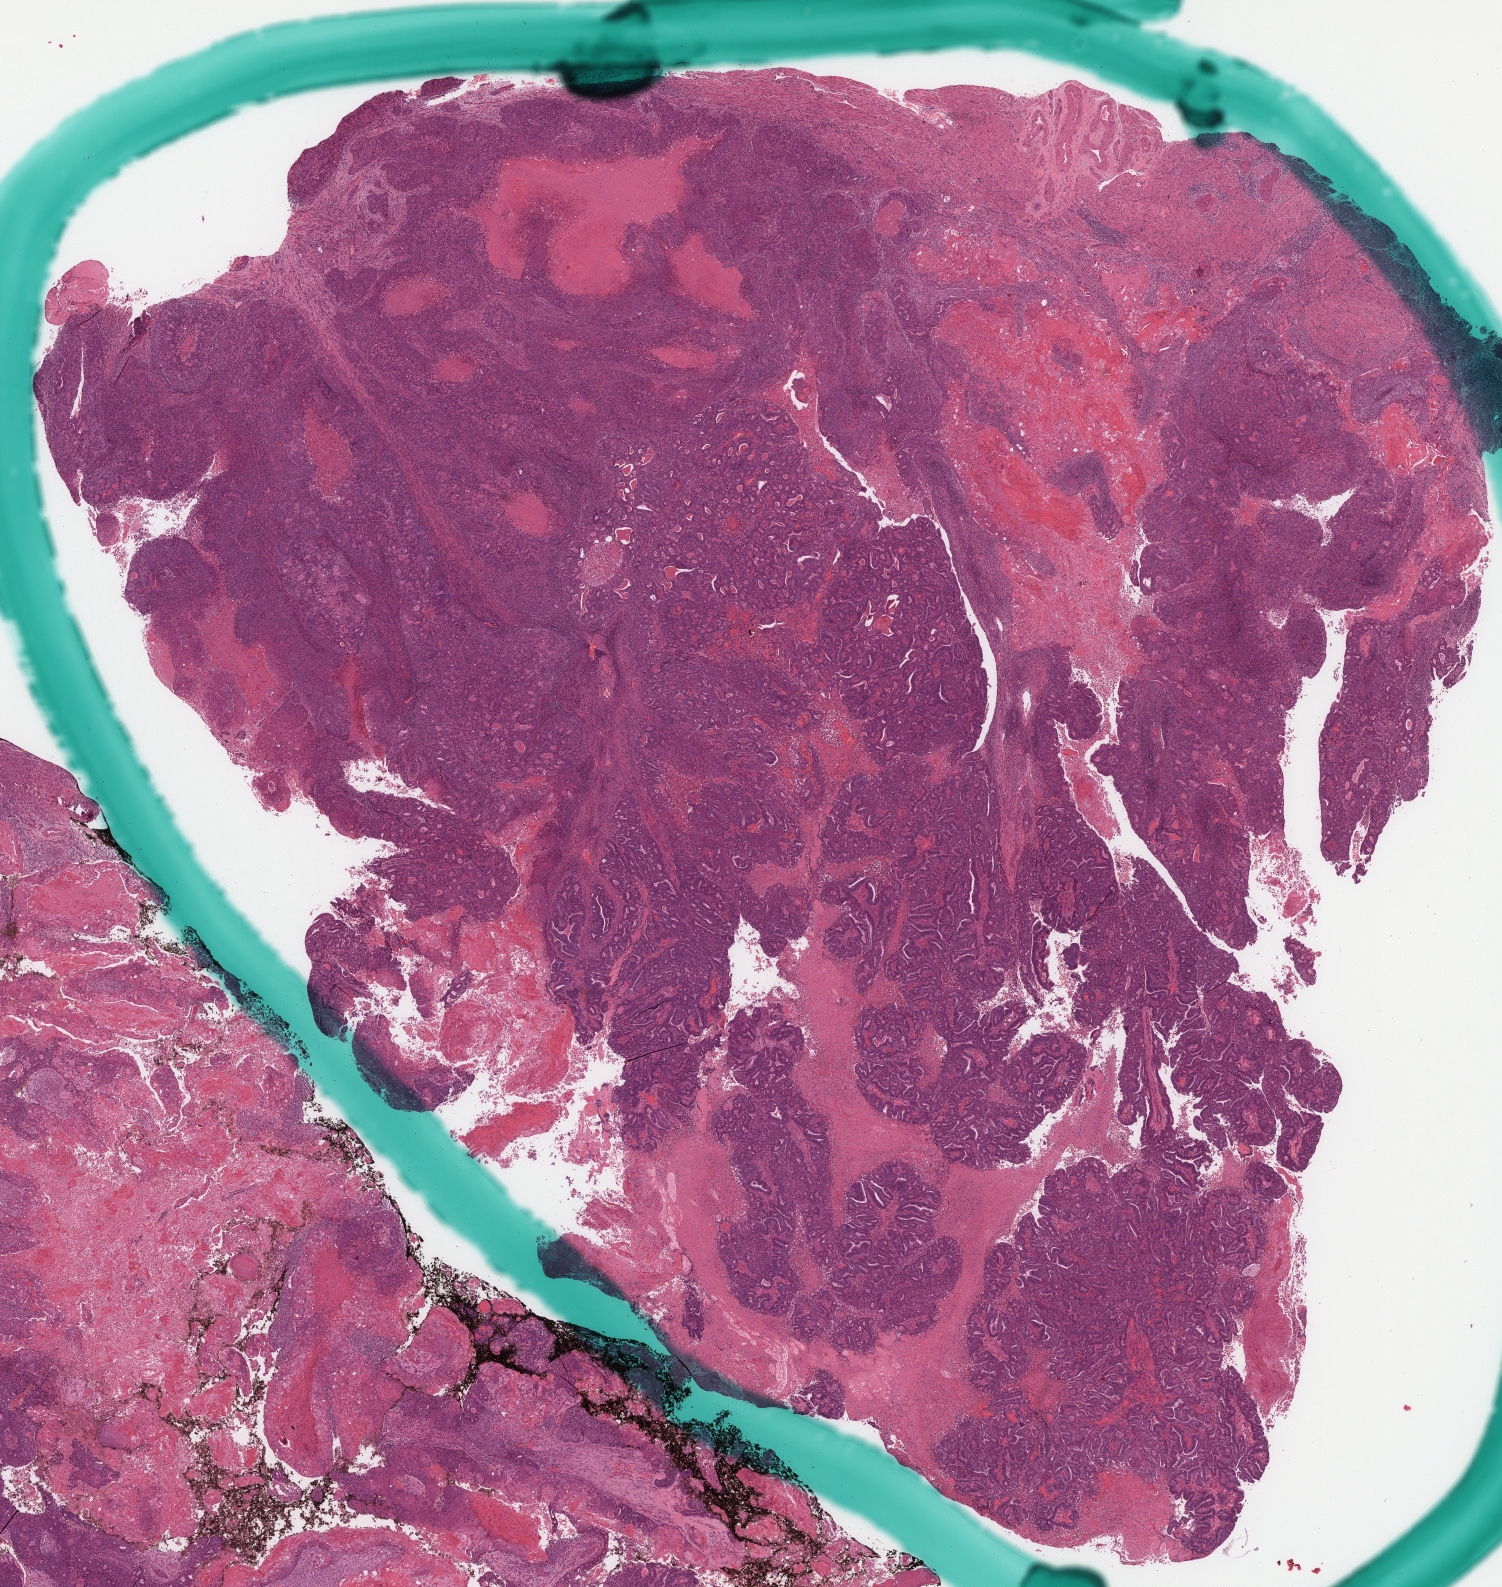
Whole-slide histology image, H&E — whole scanned area (about 12.1 x 12.8 mm, slide scanned at 40x) shown as a low-resolution overview; formalin-fixed paraffin-embedded (FFPE) diagnostic section; uterus, primary tumour sample. Patient: female, age at initial diagnosis 72 years. Histologic grade: G3 (poorly differentiated).
* FIGO stage: II
* pathologic diagnosis: Endometrioid adenocarcinoma, NOS (endometrium)